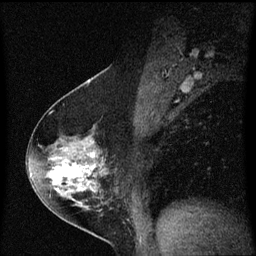
Breast MRI (dynamic contrast-enhanced), one sagittal slice; position 35 of 60 along the scan axis; dynamic contrast-enhanced series, image 2 of 3 at this slice position (ordered by acquisition); 1.5 T; TE 4.2 ms, TR 8.4 ms; 2 mm slice thickness; 256 × 256 image matrix, field of view 200 × 200 mm. Patient: female, 54 years. From the clinical record (not read from this slice): setting: breast cancer imaged before/during neoadjuvant chemotherapy; receptor status: HER2-positive.
Outlined on this slice (semi-automatically segmented with operator editing):
- analysis volume of interest (the breast-tissue region the enhancement analysis was run in; not a lesion): bounding box <32,124,119,213> (left, top, right, bottom; pixels)
- tumour enhancement mask (voxels above the 70 % enhancement threshold inside the analysis volume of interest): <50,142,97,193>